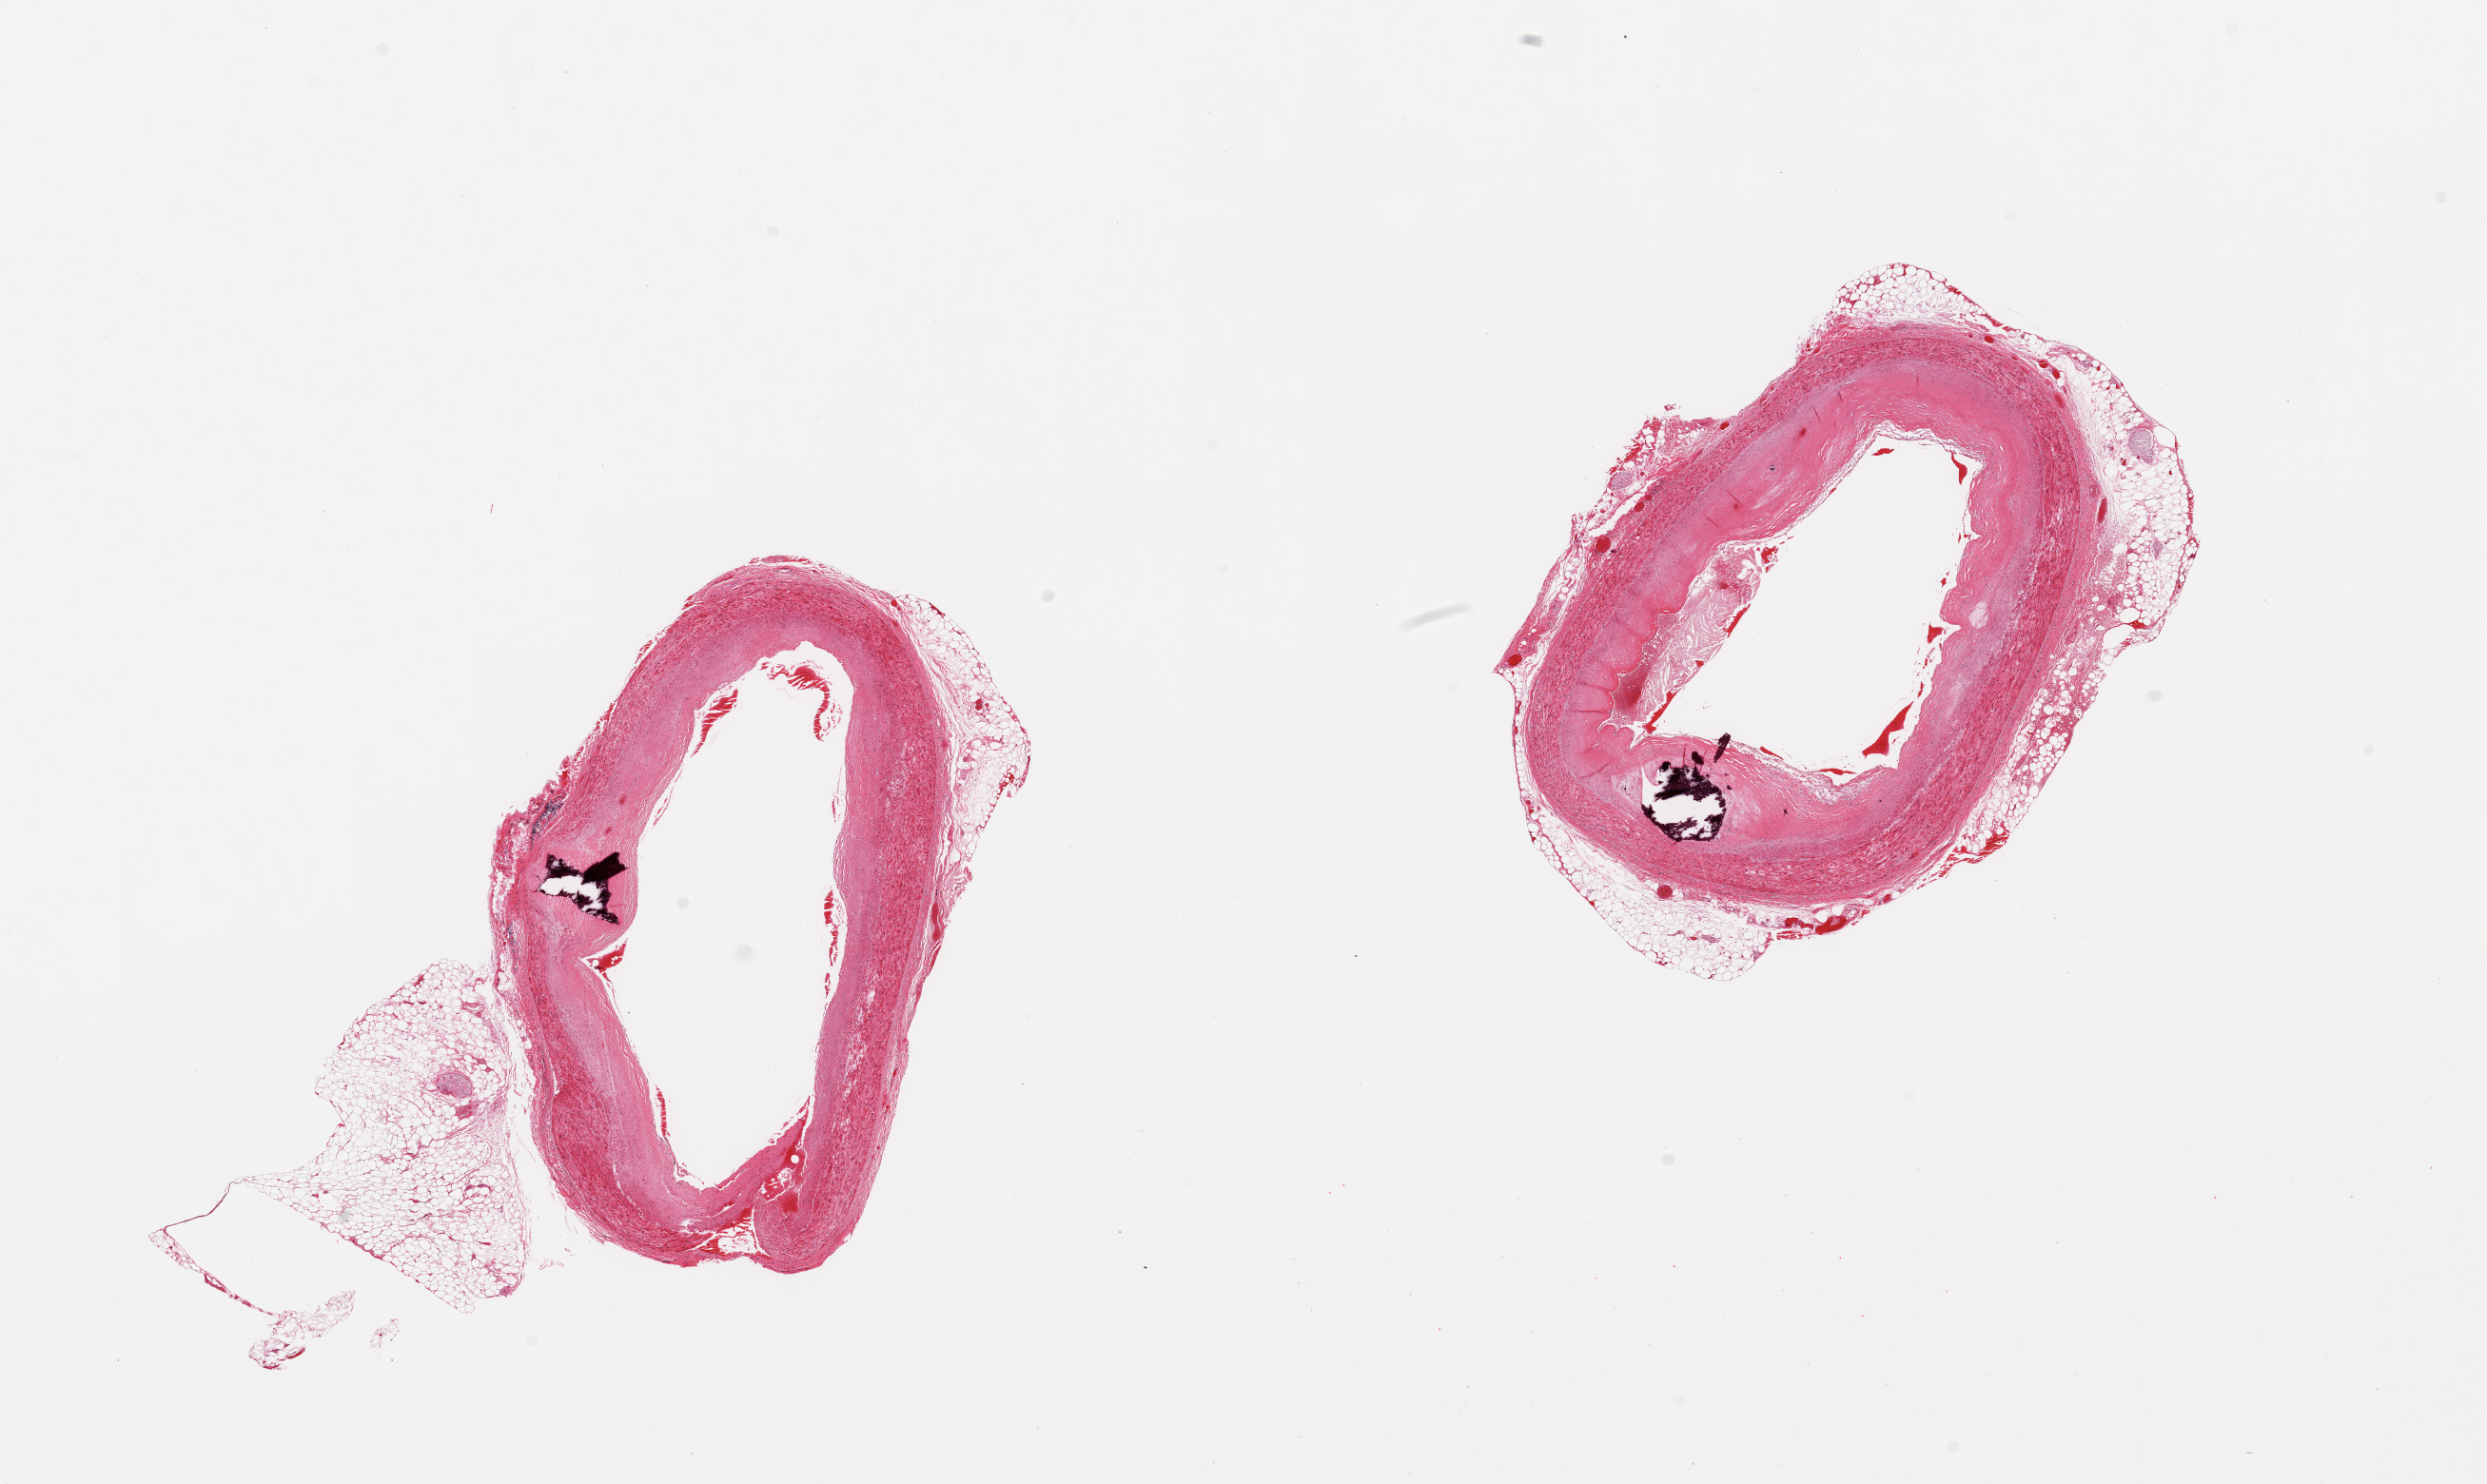
Digitized haematoxylin and eosin-stained section, brightfield — low-resolution overview of the scanned area, about 20.7 x 12.3 mm (slide scanned at 20x). PAXgene-fixed paraffin-embedded (PFPE) section. Sampled site (target tissue): coronary artery. Donor tissue sample. Donor sex: male.
Reviewer comment on this tissue sample: 2 pieces, calcifying ~30% occlusive atherosis.